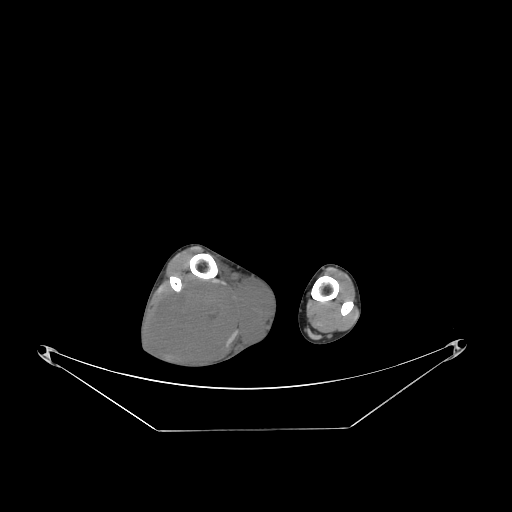
CT of an extremity soft-tissue mass (from a PET/CT study), one axial slice; position 66 of 267 along the scan axis; reconstruction kernel STANDARD; soft-tissue window (W 400 / L 40 HU); 3.75 mm slice thickness; 512 × 512 image matrix, field of view 500 × 500 mm. Male patient. Case-level facts recorded for this patient, not image findings: histological type: liposarcoma - round cell; grade: high; site of the primary tumour: right calf.
Structures marked on this image (expert contour drawn on MRI and transferred to this co-registered scan by the dataset authors):
- gross tumour volume (mass): bounding box <151,274,275,369> (left, top, right, bottom; pixels)